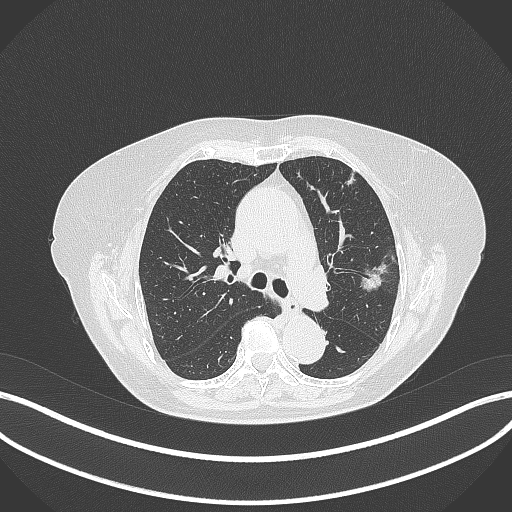
Chest CT, one axial slice. Slice 212 of 316 in the series (ordered by position). 120 kVp. Lung window (W 1500 / L -600 HU). 1 mm slice thickness. 512 × 512 image matrix. Patient: female, 75 years. From the clinical record (not read from this slice): clinical TNM (as recorded): T1c N0 M0.
Annotated regions visible in this slice (rectangle marked by the reading radiologist):
- lung tumour (recorded histology: adenocarcinoma): bounding box <360,261,387,296> (left, top, right, bottom; pixels)